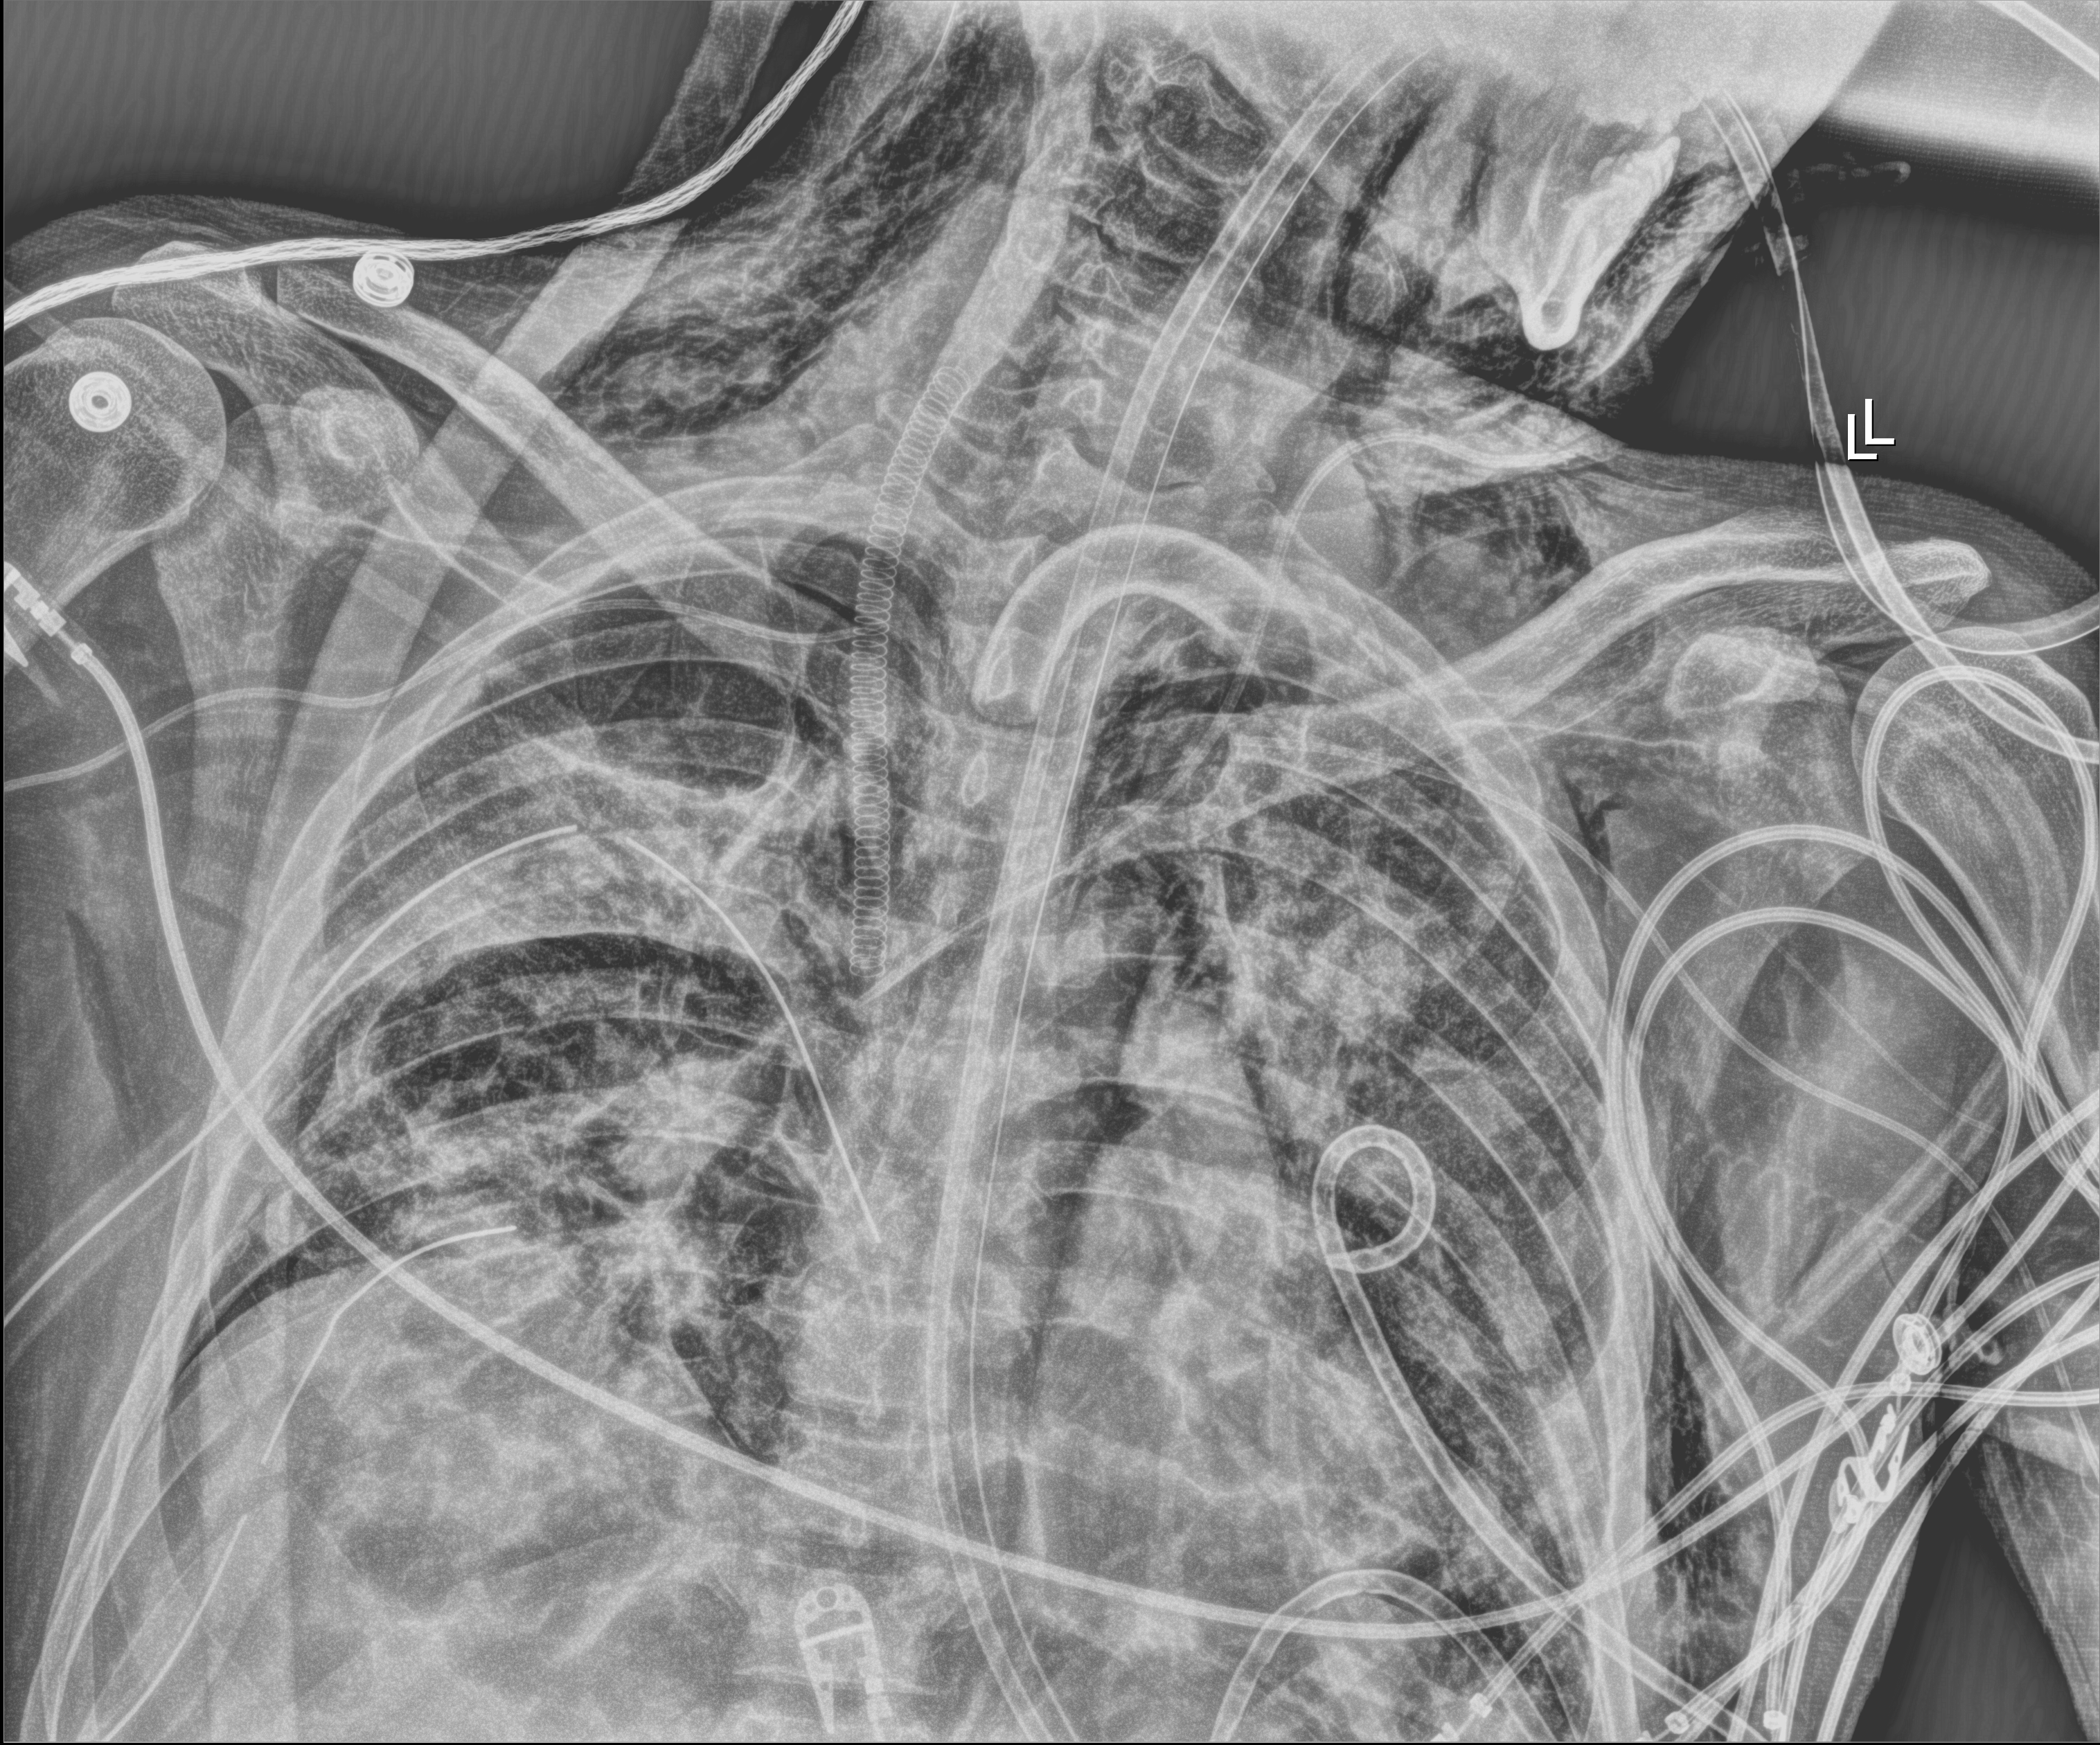
Bedside chest radiograph (digital radiography), anteroposterior (AP) projection. Patient hospitalised with COVID-19, aged 18–59 years.
From the hospital-stay record, not from the radiograph (when in the stay this image was taken is not recorded):
- other chronic lung disease (admission record): no
- chronic kidney disease (admission record): no
- mechanically ventilated during this hospital stay: yes